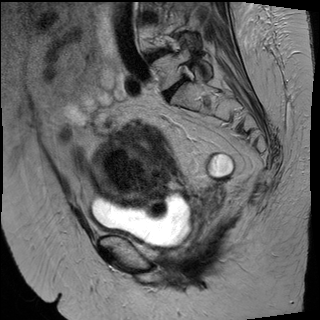
Pelvic MRI for cervical cancer, one sagittal slice; slice 29 of 50 in the series (ordered by position); T2-weighted; 1.5 T; TE 89 ms, TR 4880 ms; 4 mm slice thickness; 320 × 320 image matrix. Female patient, age 50 years.
Structures marked on this image (manually delineated by an expert):
- uterus and cervix: box from (x=88, y=124) to (x=175, y=220) px